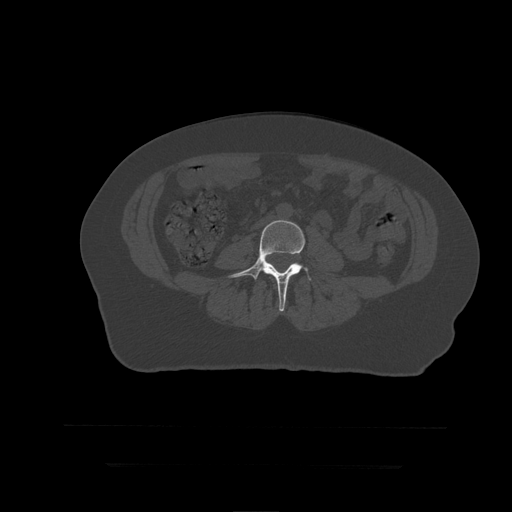
CT including the spine, one axial slice. Slice 97 of 399 in the series (ordered by position). Reconstruction kernel STANDARD. 120 kVp. Bone window (W 1800 / L 400 HU). 1.25 mm slice thickness. 512 × 512 image matrix, field of view 450 × 450 mm. Patient age 41 years. Case-level facts recorded for this patient, not image findings: primary cancer: breast.
Annotated regions visible in this slice (semi-automatically segmented with operator editing):
- L4 vertebra: bounding box <229,220,312,312> (left, top, right, bottom; pixels)